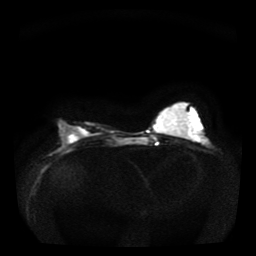
Breast MRI, one axial slice. Slice 13 of 36 in the series (ordered by position). Diffusion-weighted series; image 2 of 4 stored at this slice position (different b-values; order by instance number). 1.5 T. 256 × 256 image matrix, field of view 330 × 330 mm. Female patient.
Structures marked on this image (outlined manually by an expert reader):
- tumour on diffusion-weighted imaging: bounding box (x1, y1, x2, y2) in pixels: (68, 136, 76, 143)